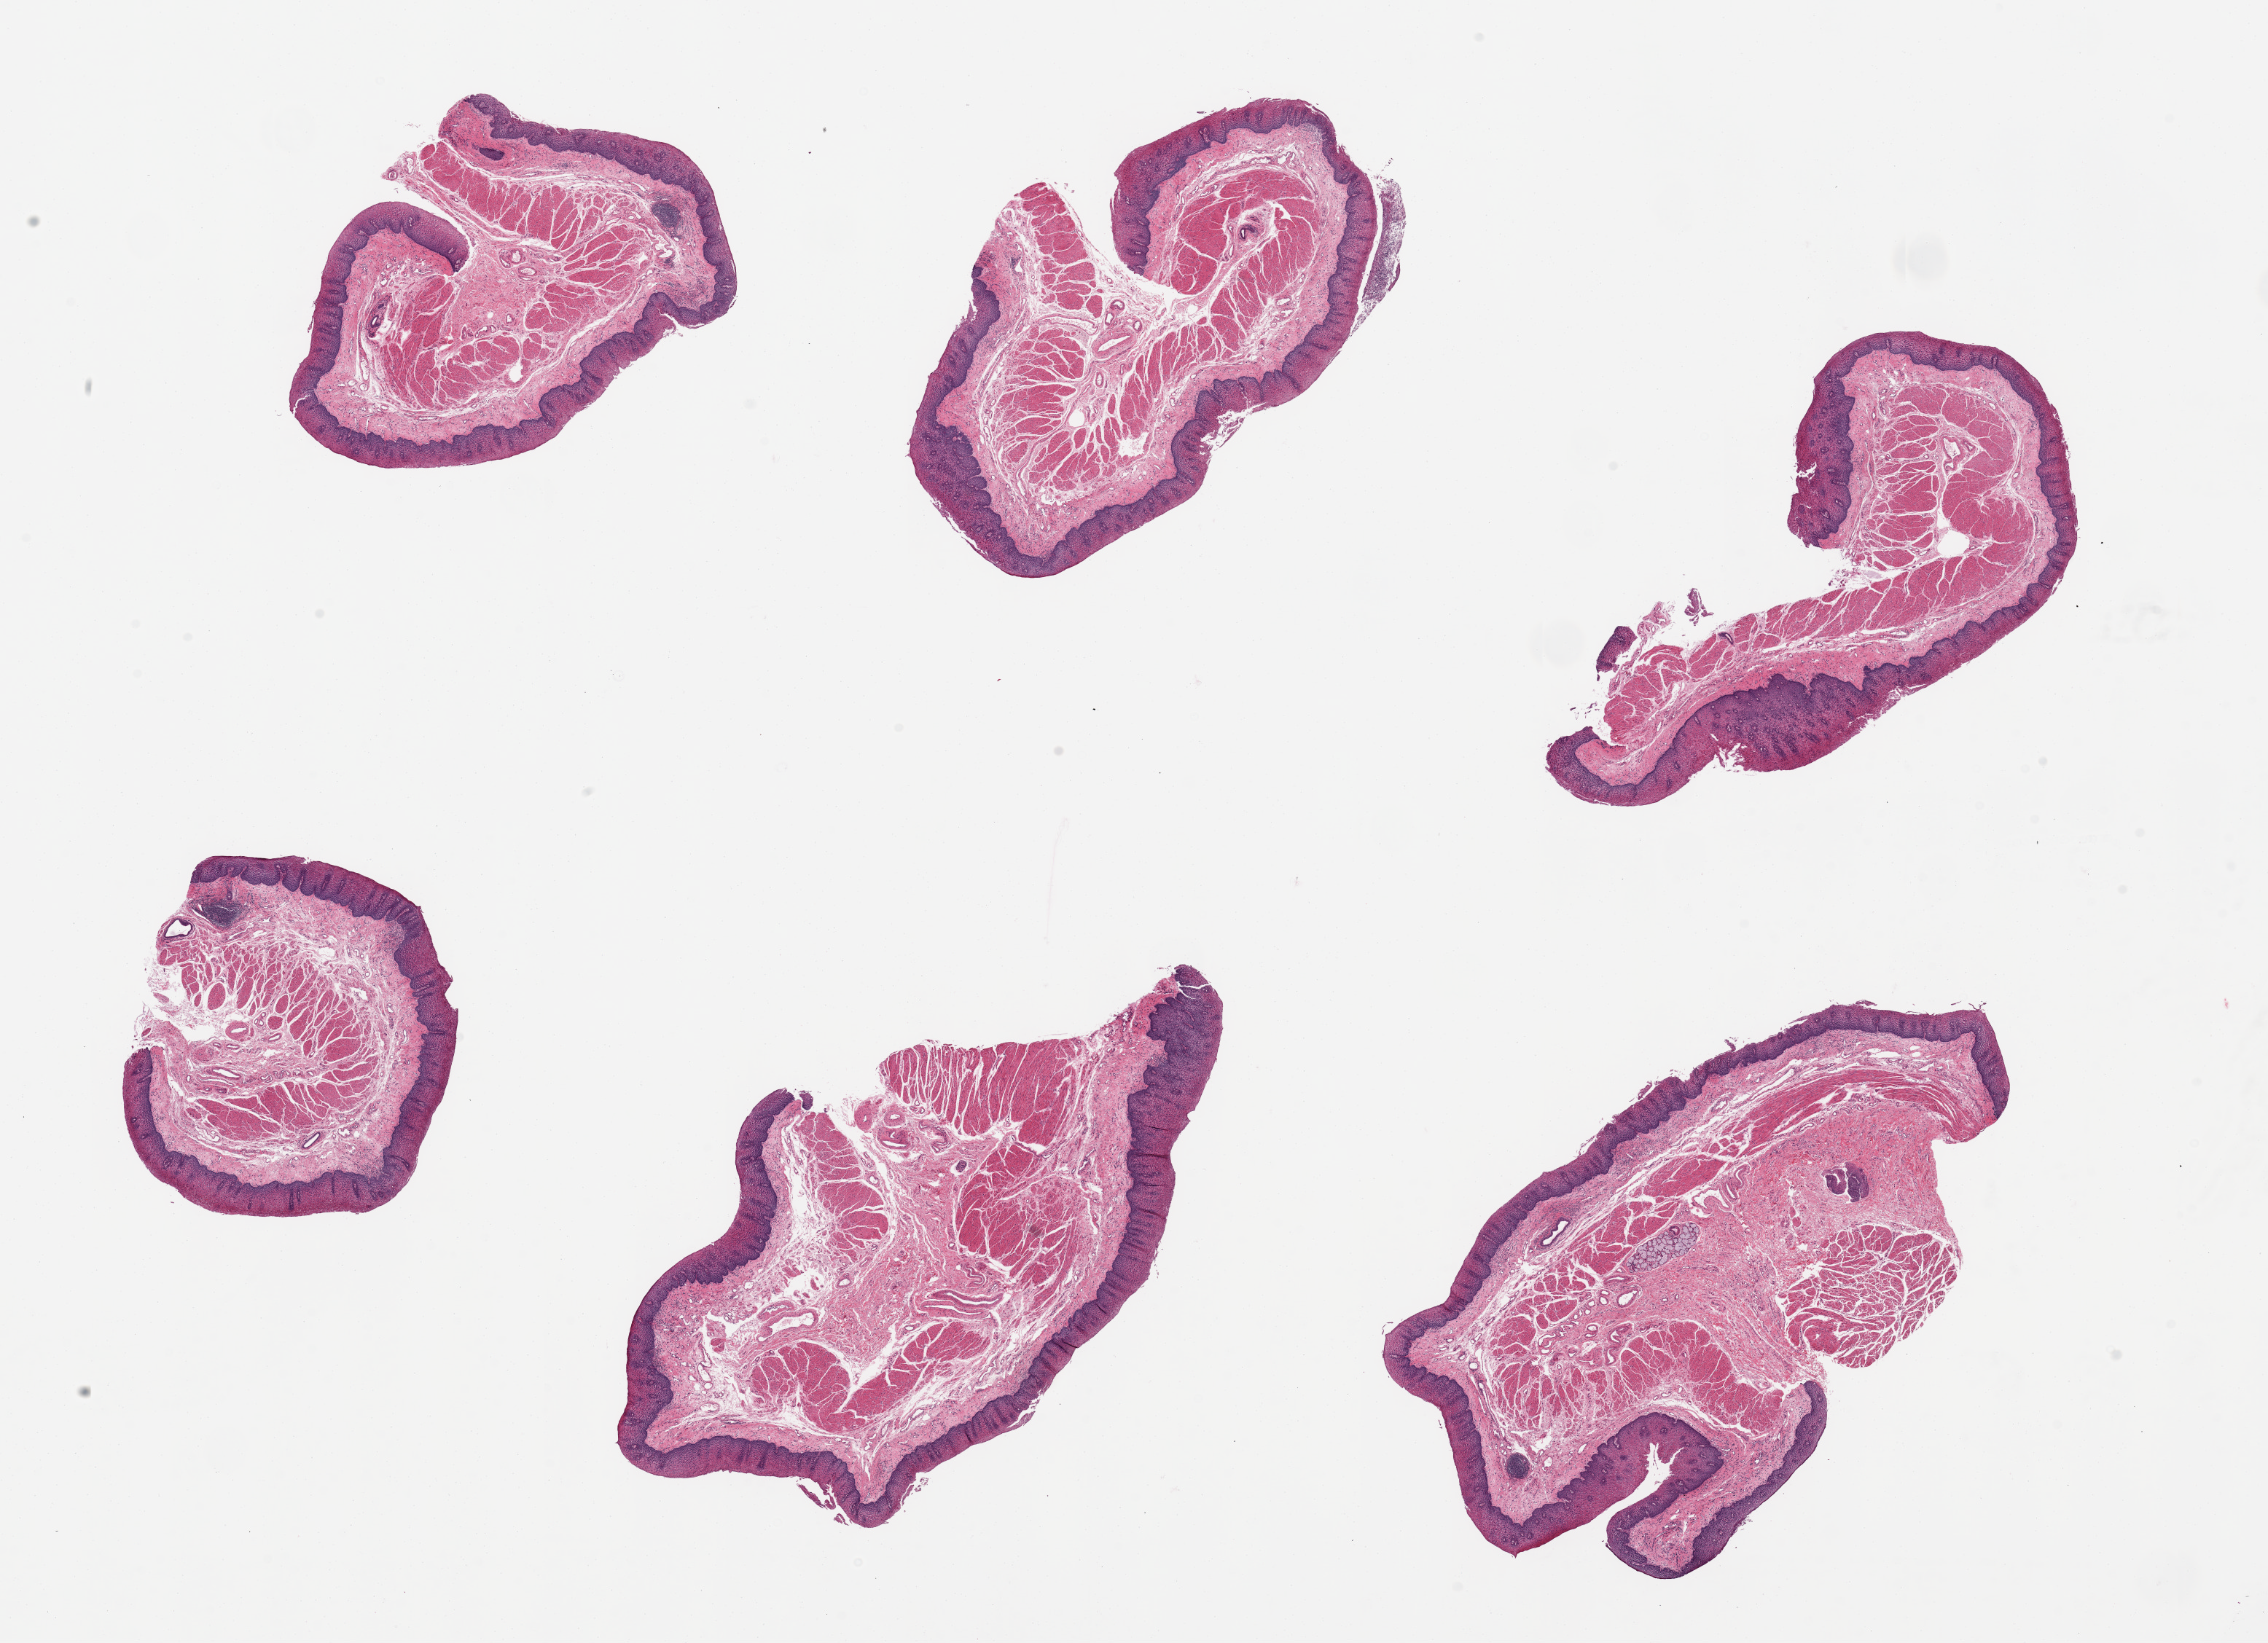
Whole-slide image, haematoxylin and eosin stain, low-resolution overview of the scanned area, about 24.6 x 17.8 mm. PAXgene-fixed, paraffin-embedded tissue. Sampled site (target tissue): esophageal mucous membrane. Tissue donor sample. Donor sex: female.
Review note (as recorded): 6 pieces, up to 8x5mm; squamous mucosa up to ~20% thickness.